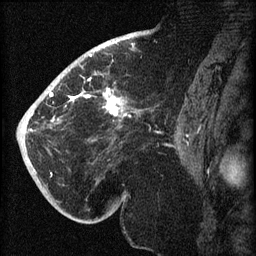
Breast MRI (dynamic contrast-enhanced), one sagittal slice; position 40 of 60 along the scan axis; dynamic contrast-enhanced series, image 2 of 3 at this slice position (ordered by acquisition); 1.5 T; TE 4.2 ms, TR 8.2 ms; 2 mm slice thickness; 256 × 256 image matrix, field of view 180 × 180 mm. Patient: female, 71 years.
Outlined on this slice (semi-automatic segmentation, software-assisted and operator-edited):
- analysis volume of interest (the breast-tissue region the enhancement analysis was run in; not a lesion): bounding box <40,72,147,196> (left, top, right, bottom; pixels)
- tumour enhancement mask (voxels above the 70 % enhancement threshold inside the analysis volume of interest): <49,78,121,122>